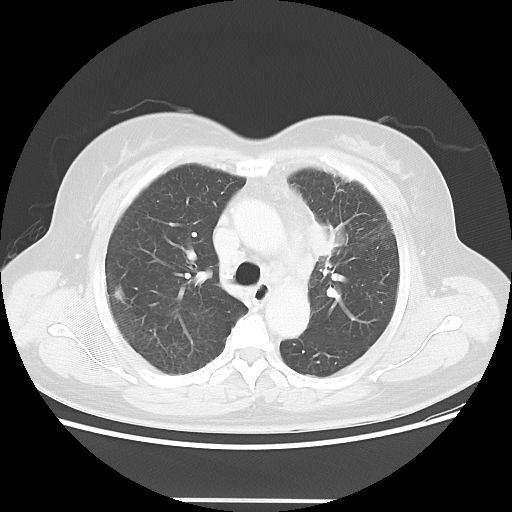
Chest CT, one axial slice; slice 38 of 52 in the series (ordered by position); reconstruction kernel LUNG; 120 kVp; lung window (W 1500 / L -600 HU); 5 mm slice thickness; 512 × 512 image matrix, field of view 382 × 382 mm. Patient: female, 52 years. Case-level facts recorded for this patient, not image findings: clinical TNM (as recorded): T2 N3 M0.
Annotated regions visible in this slice (rectangle marked by the reading radiologist):
- lung tumour (recorded histology: adenocarcinoma): bounding box (x1, y1, x2, y2) in pixels: (301, 203, 348, 259)